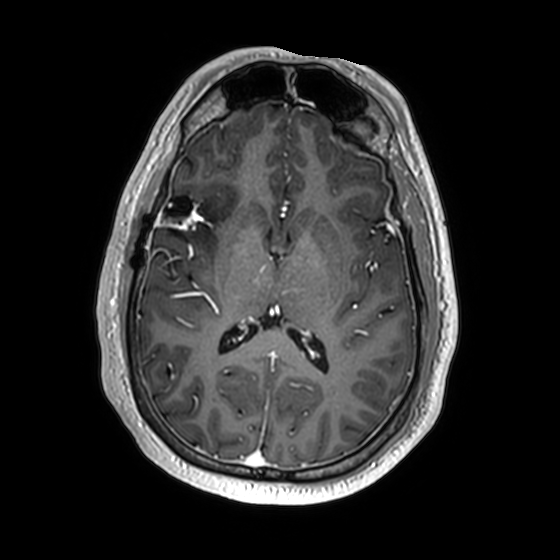
Brain MRI from a brain-tumour surgery series, one axial slice; slice 85 of 174 in the series (ordered by position); T1-weighted post-contrast; 1 mm slice thickness; 560 × 560 image matrix, field of view 256 × 256 mm. From the clinical record (not read from this slice): histopathology: Astrocytoma; WHO grade: 2; IDH mutation: yes; tumour location: Right Insular.
Structures marked on this image (manually delineated by an expert):
- previous resection cavity: bounding box (x1, y1, x2, y2) in pixels: (162, 195, 210, 224)